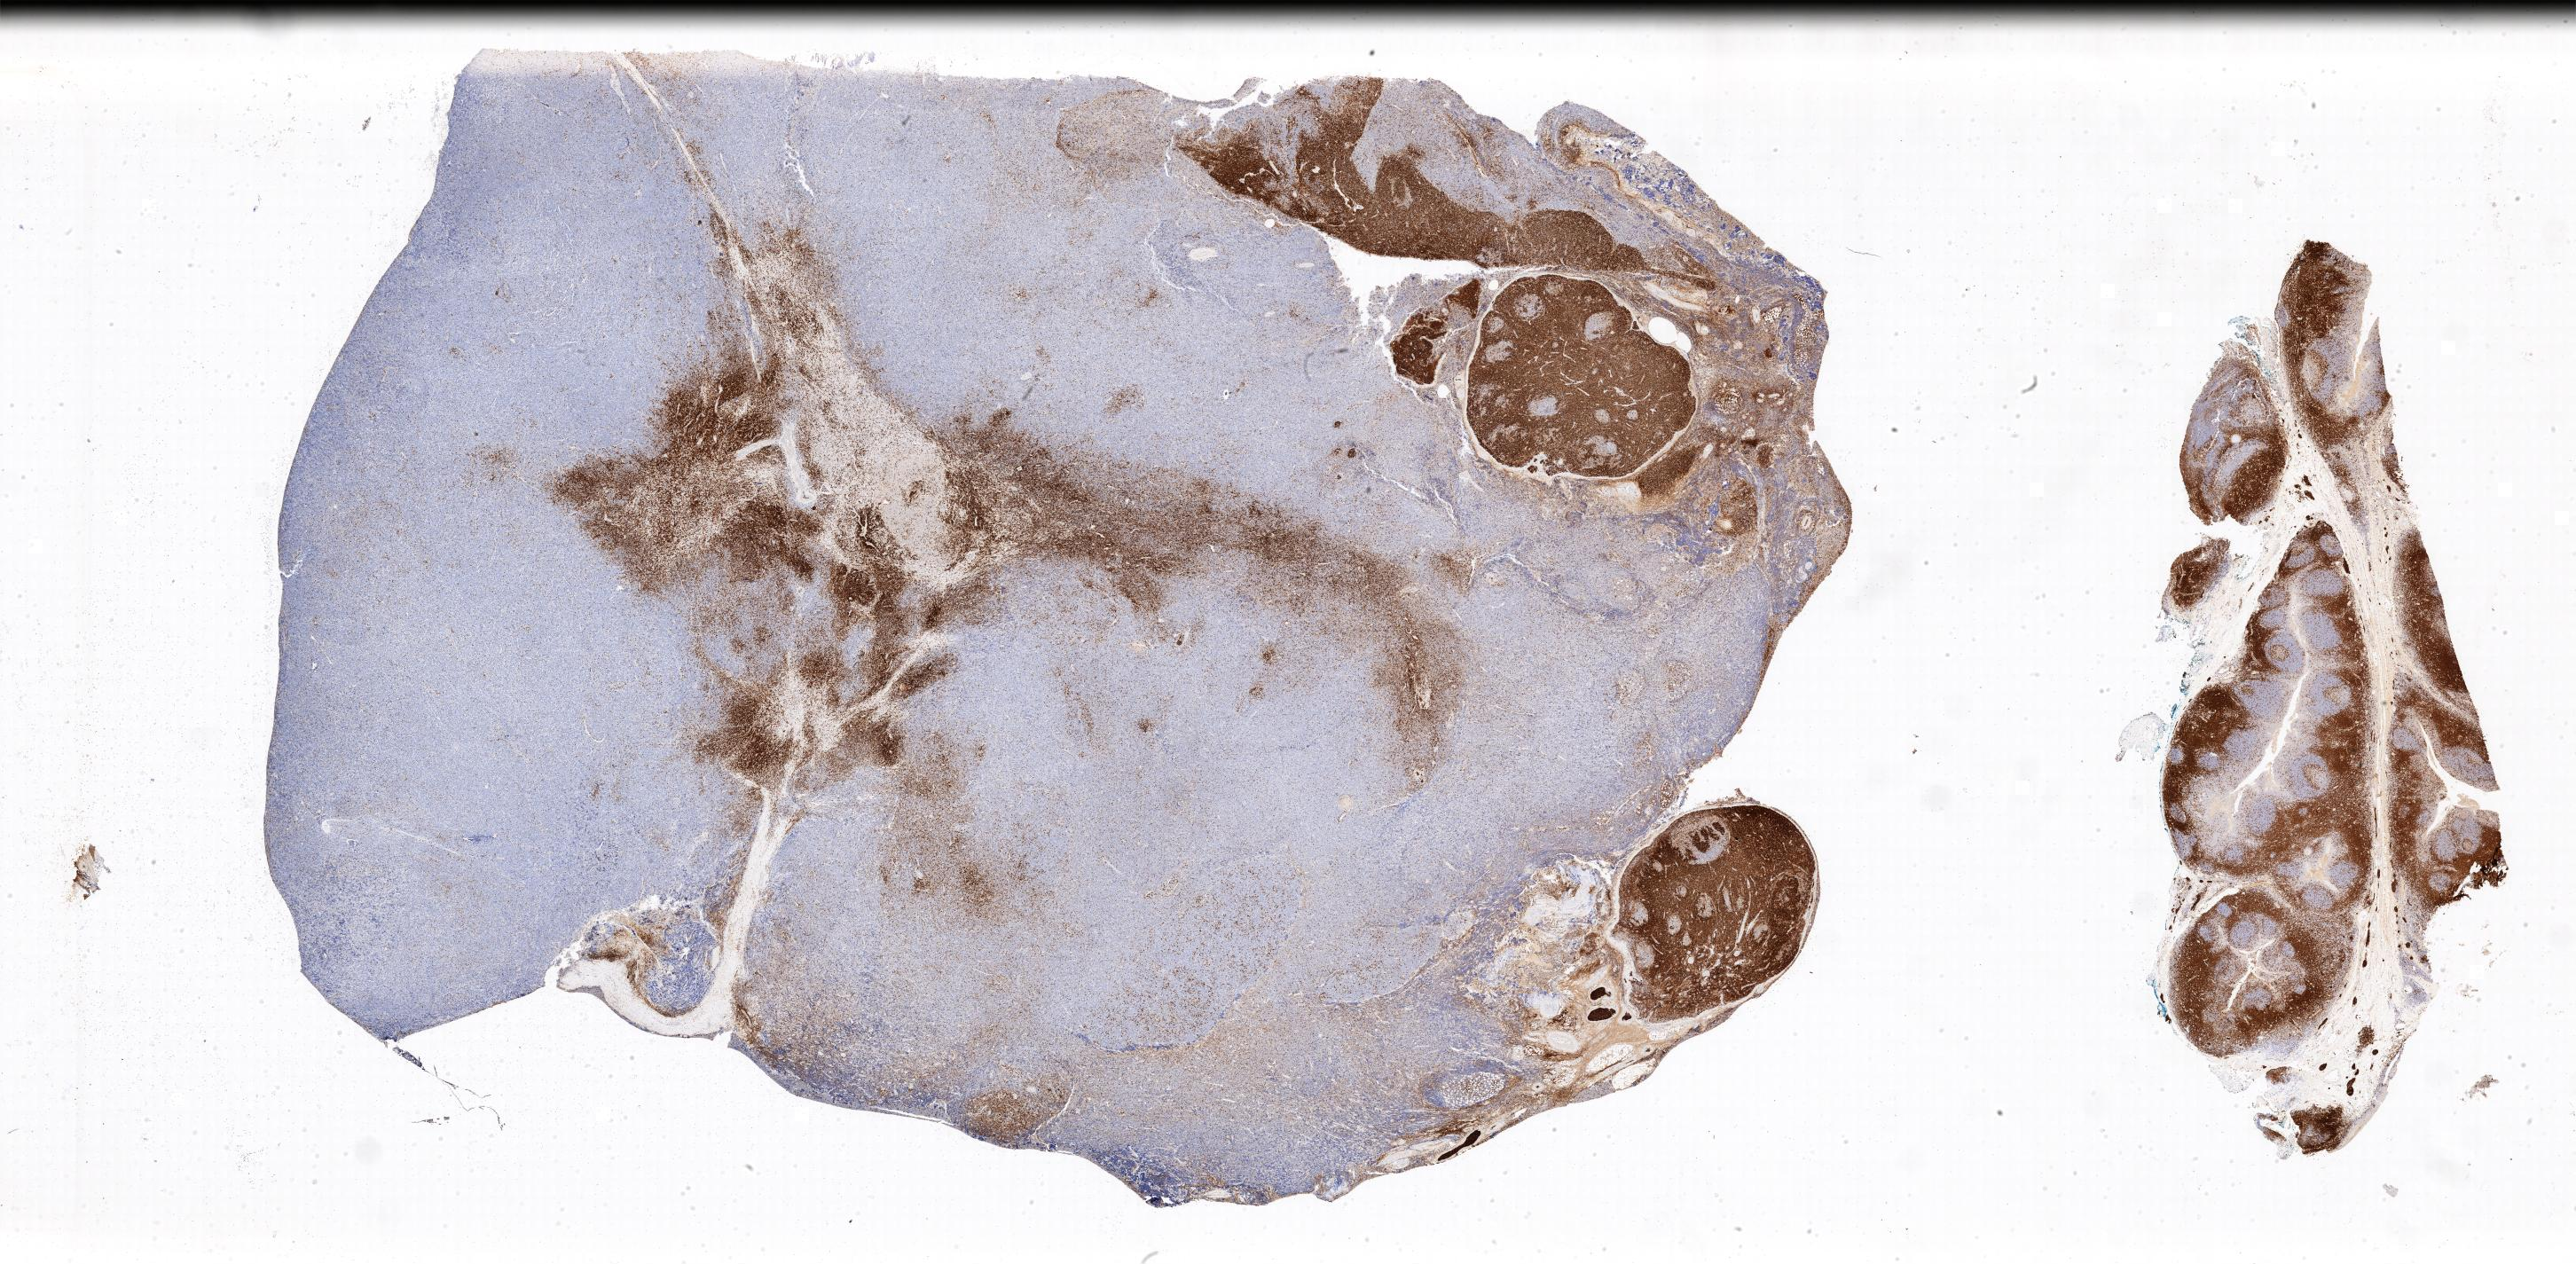
Whole-slide image, immunohistochemical stain for CD3, whole scanned area shown as a low-resolution overview; specimen: tumor tissue; site: lymph node of head and neck. Male patient; age at initial diagnosis 3 years.
Diagnosis: Burkitt lymphoma, NOS.